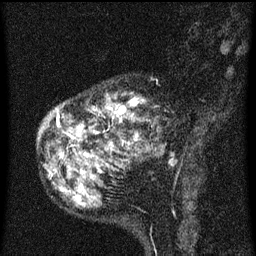
Breast MRI (dynamic contrast-enhanced), one sagittal slice. Position 19 of 60 along the scan axis. Dynamic contrast-enhanced series, image 2 of 3 at this slice position (ordered by acquisition). 1.5 T. TE 4.2 ms, TR 8 ms. 256 × 256 image matrix. Patient: female, 55 years.
Structures marked on this image (semi-automatically segmented with operator editing):
- analysis volume of interest (the breast-tissue region the enhancement analysis was run in; not a lesion): bounding box (x1, y1, x2, y2) in pixels: (42, 80, 169, 155)
- tumour enhancement mask (voxels above the 70 % enhancement threshold inside the analysis volume of interest): (57, 98, 145, 147)